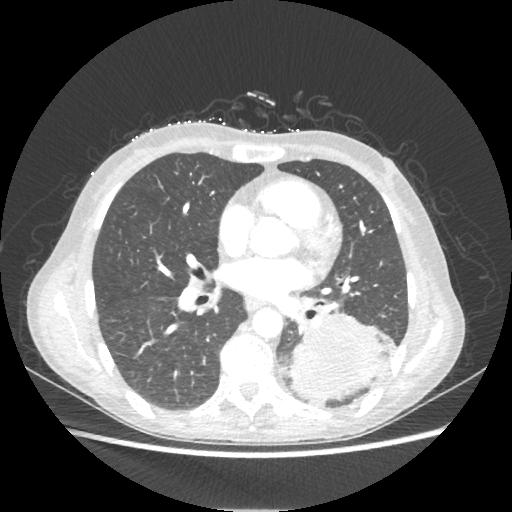
Chest CT, one axial slice. Slice 106 of 221 in the series (ordered by position). 80 kVp. Lung window (W 1500 / L -600 HU). 512 × 512 image matrix, field of view 360 × 360 mm. Patient: female, 53 years. Case-level facts recorded for this patient, not image findings: clinical TNM (as recorded): T3 N0 M0.
Structures marked on this image (rectangle marked by the reading radiologist):
- lung tumour (recorded histology: adenocarcinoma): bounding box <291,313,387,400> (left, top, right, bottom; pixels)